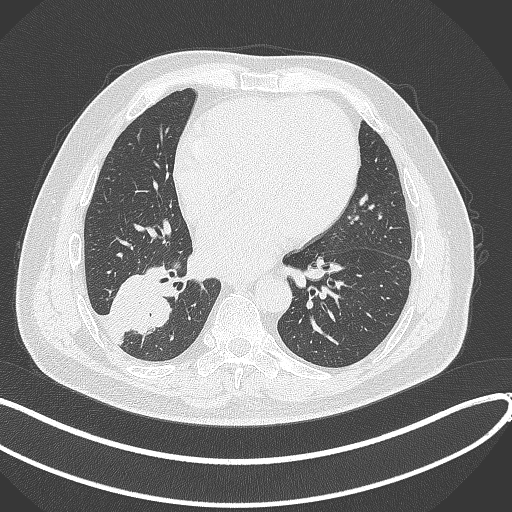
Chest CT, one axial slice. Position 148 of 360 along the scan axis. Reconstruction kernel B70f. 120 kVp. Lung window (W 1500 / L -600 HU). 1 mm slice thickness. 512 × 512 image matrix. Patient: male, 59 years.
Outlined on this slice (rectangle marked by the reading radiologist):
- lung tumour (recorded histology: adenocarcinoma): box from (x=104, y=258) to (x=173, y=339) px